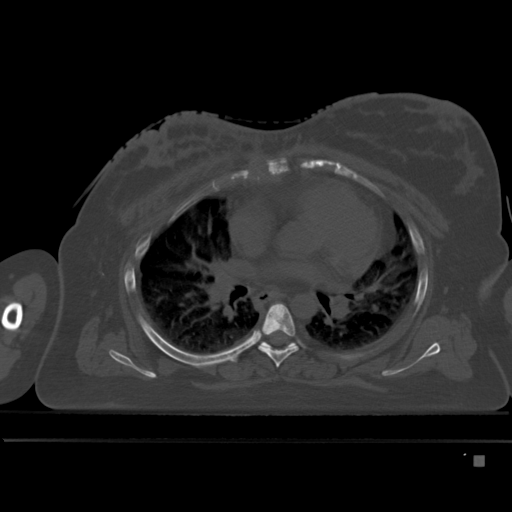
CT including the spine, one axial slice. Slice 316 of 495 in the series (ordered by position). Bone window (W 1800 / L 400 HU). 1.5 mm slice thickness. 512 × 512 image matrix. Patient: female, 33 years. Case-level facts recorded for this patient, not image findings: primary cancer: breast; vertebrae with lytic lesions (as recorded): T1.
Outlined on this slice (semi-automatic segmentation, software-assisted and operator-edited):
- T5 vertebra: bounding box (x1, y1, x2, y2) in pixels: (259, 303, 298, 368)
- T6 vertebra: (259, 341, 298, 348)